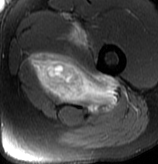
MRI of an extremity soft-tissue mass, one axial slice. Position 62 of 70 along the scan axis. T2-weighted fat-saturated. MR volume resampled by the dataset authors to the PET/CT grid (not the native acquisition matrix). 158 × 164 image matrix. Male patient. Case-level facts recorded for this patient, not image findings: histological type: extraskeletal osteosarcoma; grade: high; site of the primary tumour: left adductur.
Structures marked on this image (expert contour drawn on MRI and transferred to this co-registered scan by the dataset authors):
- gross tumour volume (mass): box from (x=29, y=23) to (x=121, y=113) px